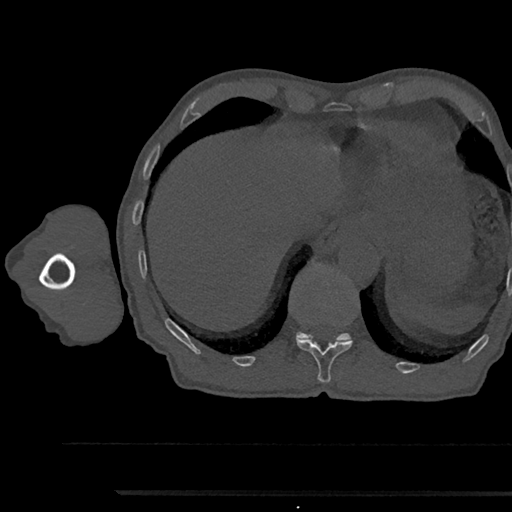
CT including the spine, one axial slice. Position 762 of 797 along the scan axis. Reconstruction kernel Br40s/3. 120 kVp. Bone window (W 1800 / L 400 HU). 512 × 512 image matrix, field of view 367 × 367 mm. Patient: male, 79 years. From the clinical record (not read from this slice): primary cancer: prostate.
Annotated regions visible in this slice (semi-automatically segmented with operator editing):
- T11 vertebra: box from (x=296, y=338) to (x=352, y=383) px
- T12 vertebra: (x=296, y=264)–(x=352, y=342)